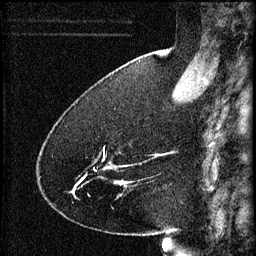
Breast MRI (dynamic contrast-enhanced), one sagittal slice. Slice 21 of 60 in the series (ordered by position). 3 images stored at this slice position (order not interpretable as contrast timing). 1.5 T. TE 4.2 ms, TR 8.2 ms. 2 mm slice thickness. 256 × 256 image matrix. Female patient, age 41 years.
Annotated regions visible in this slice (semi-automatically segmented with operator editing):
- analysis volume of interest (the breast-tissue region the enhancement analysis was run in; not a lesion): bounding box [x1, y1, x2, y2] px = [74, 148, 134, 195]
- tumour enhancement mask (voxels above the 70 % enhancement threshold inside the analysis volume of interest): [118, 182, 126, 187]